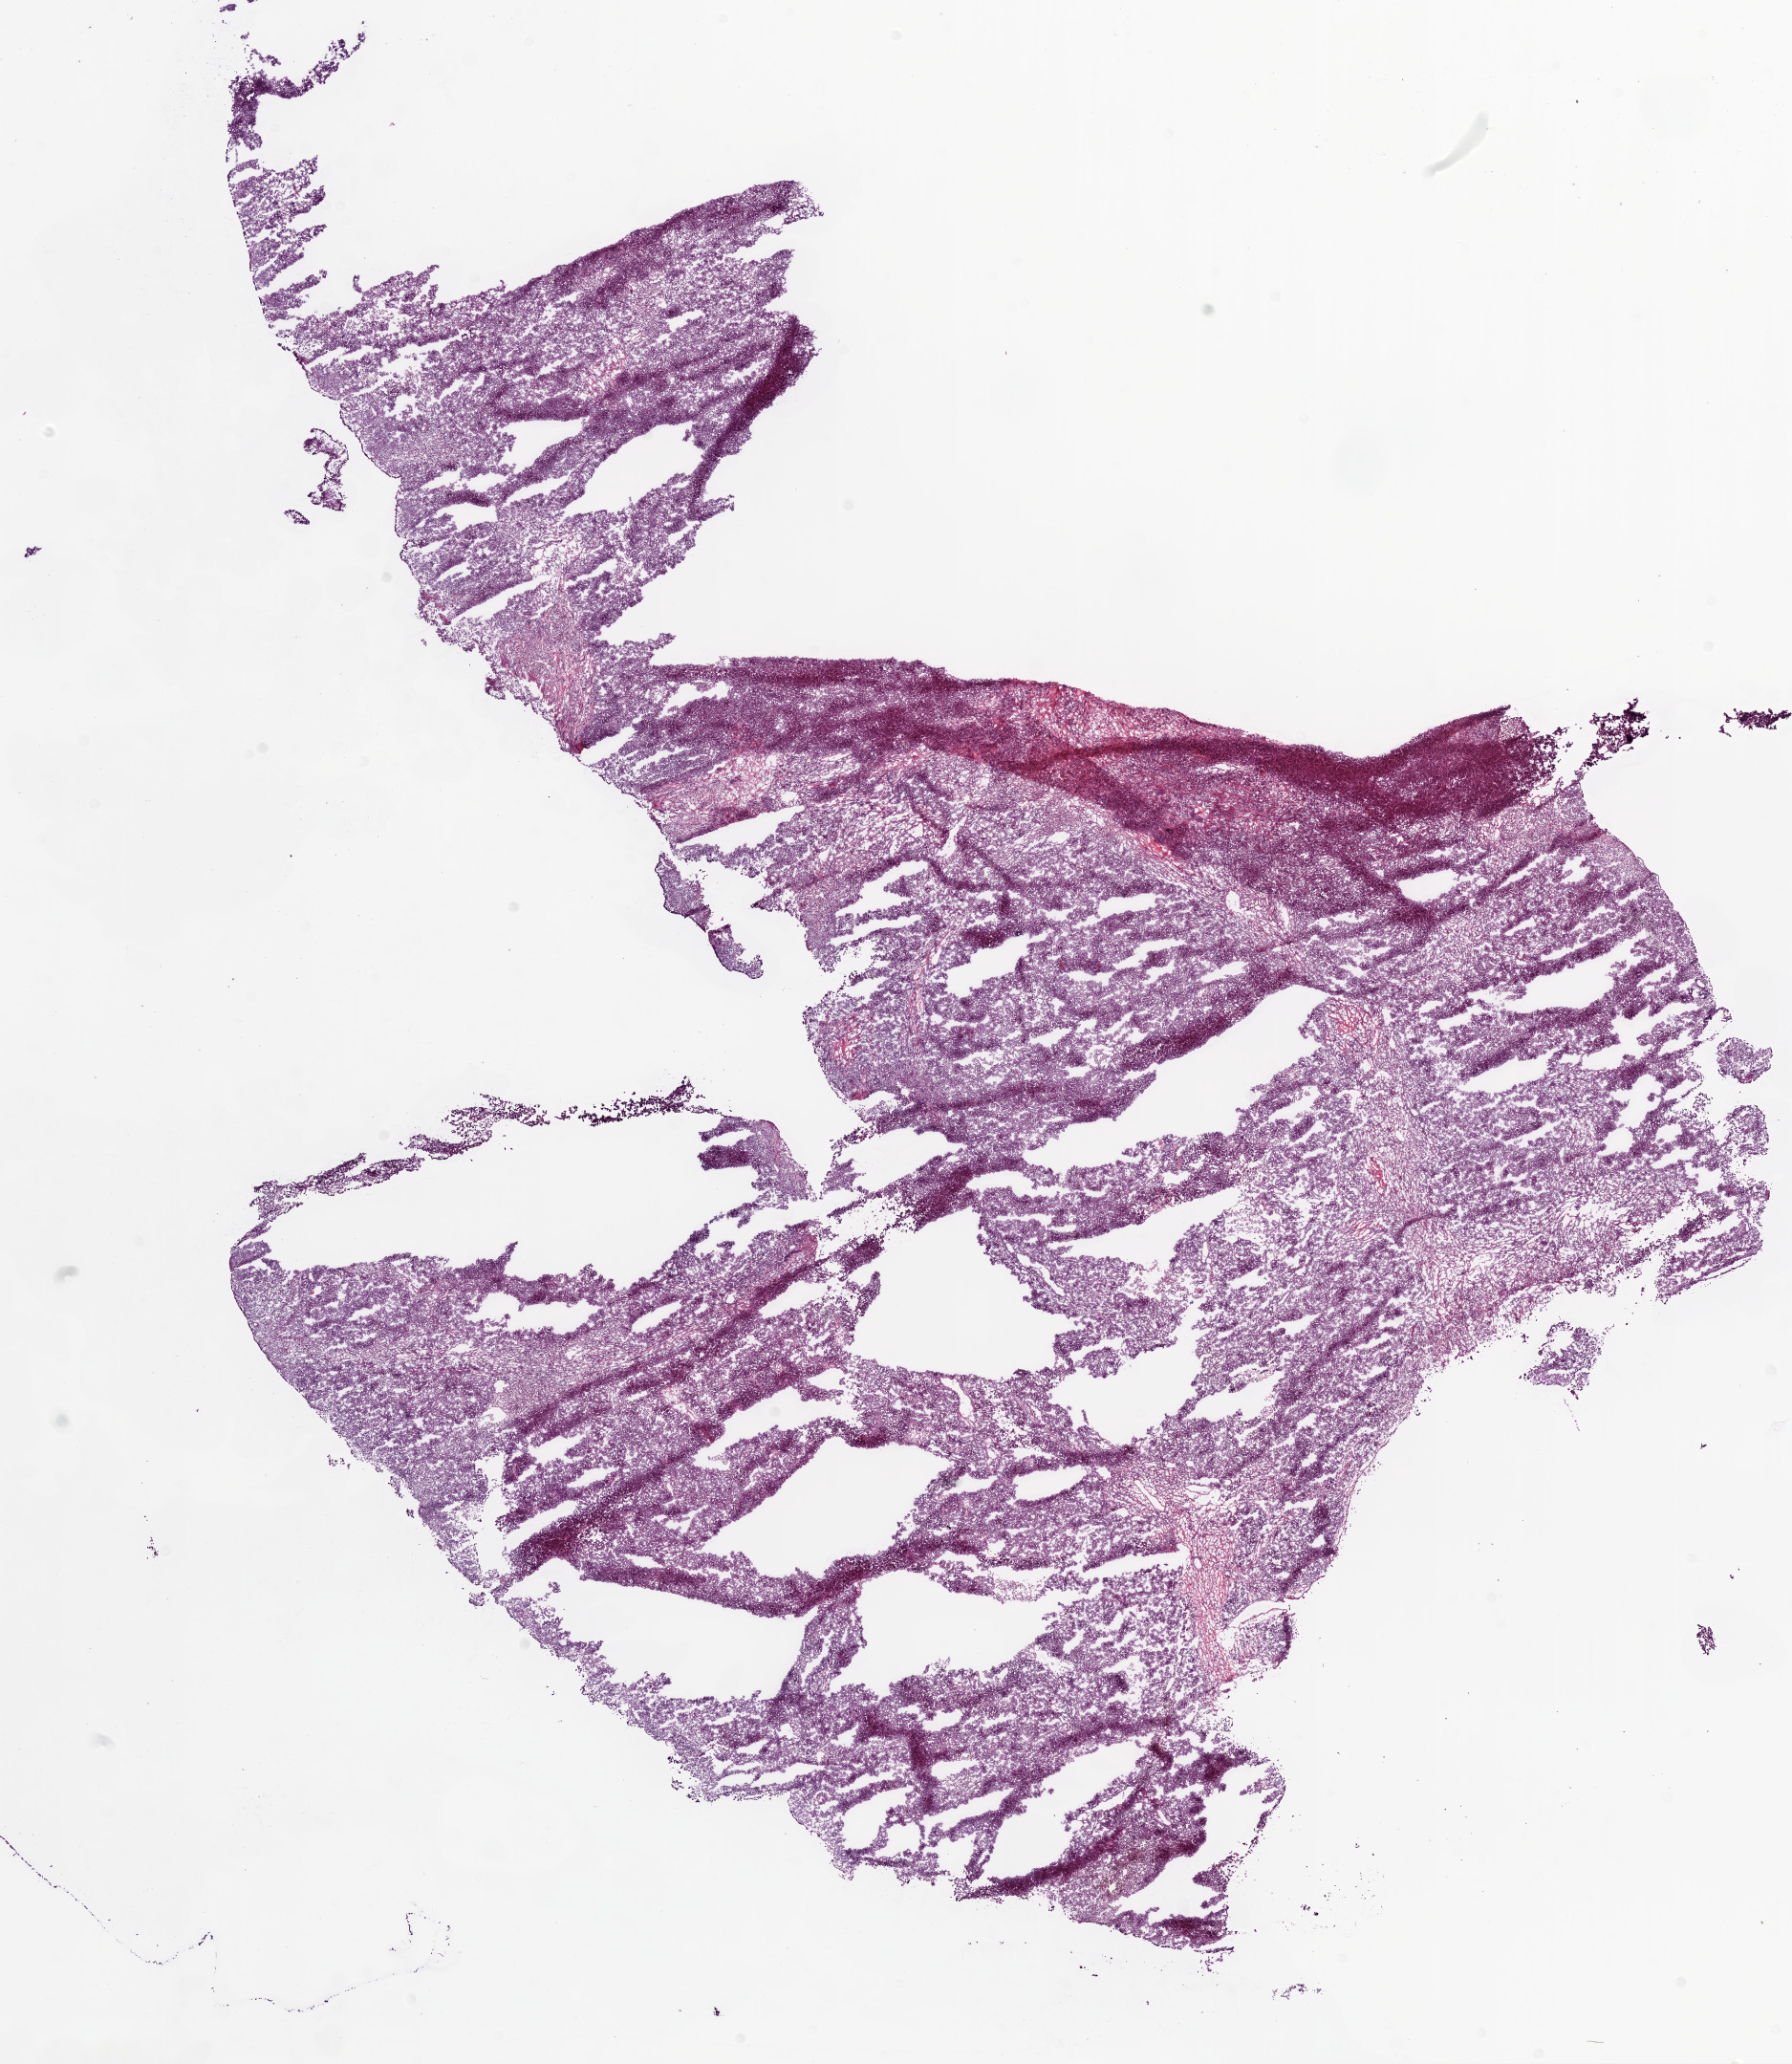
H&E-stained whole-slide image — a low-resolution overview of the entire scanned area, about 15.0 x 17.3 mm, frozen section, primary tumour sample from the ovary. Female patient; age at initial diagnosis 56 years. Histologic grade: G3 (poorly differentiated). Slide review estimates, as recorded: tumour cells 90%, tumour nuclei 90%, normal cells 0%, stromal cells 10%, necrosis 0%.
FIGO stage: IIIC. Laterality: bilateral. Diagnosis: Serous cystadenocarcinoma, NOS.